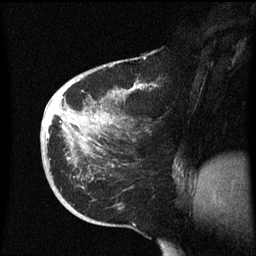
Breast MRI (dynamic contrast-enhanced), one sagittal slice. Dynamic contrast-enhanced series, image 2 of 3 at this slice position (ordered by acquisition). 1.5 T. TE 4.2 ms, TR 8.4 ms. 2.3 mm slice thickness. 256 × 256 image matrix. Female patient, age 38 years. From the clinical record (not read from this slice): setting: breast cancer imaged before/during neoadjuvant chemotherapy; receptor status: HER2-positive.
Annotated regions visible in this slice (semi-automatic segmentation, software-assisted and operator-edited):
- analysis volume of interest (the breast-tissue region the enhancement analysis was run in; not a lesion): bounding box <41,78,183,213> (left, top, right, bottom; pixels)
- tumour enhancement mask (voxels above the 70 % enhancement threshold inside the analysis volume of interest): <53,84,142,149>